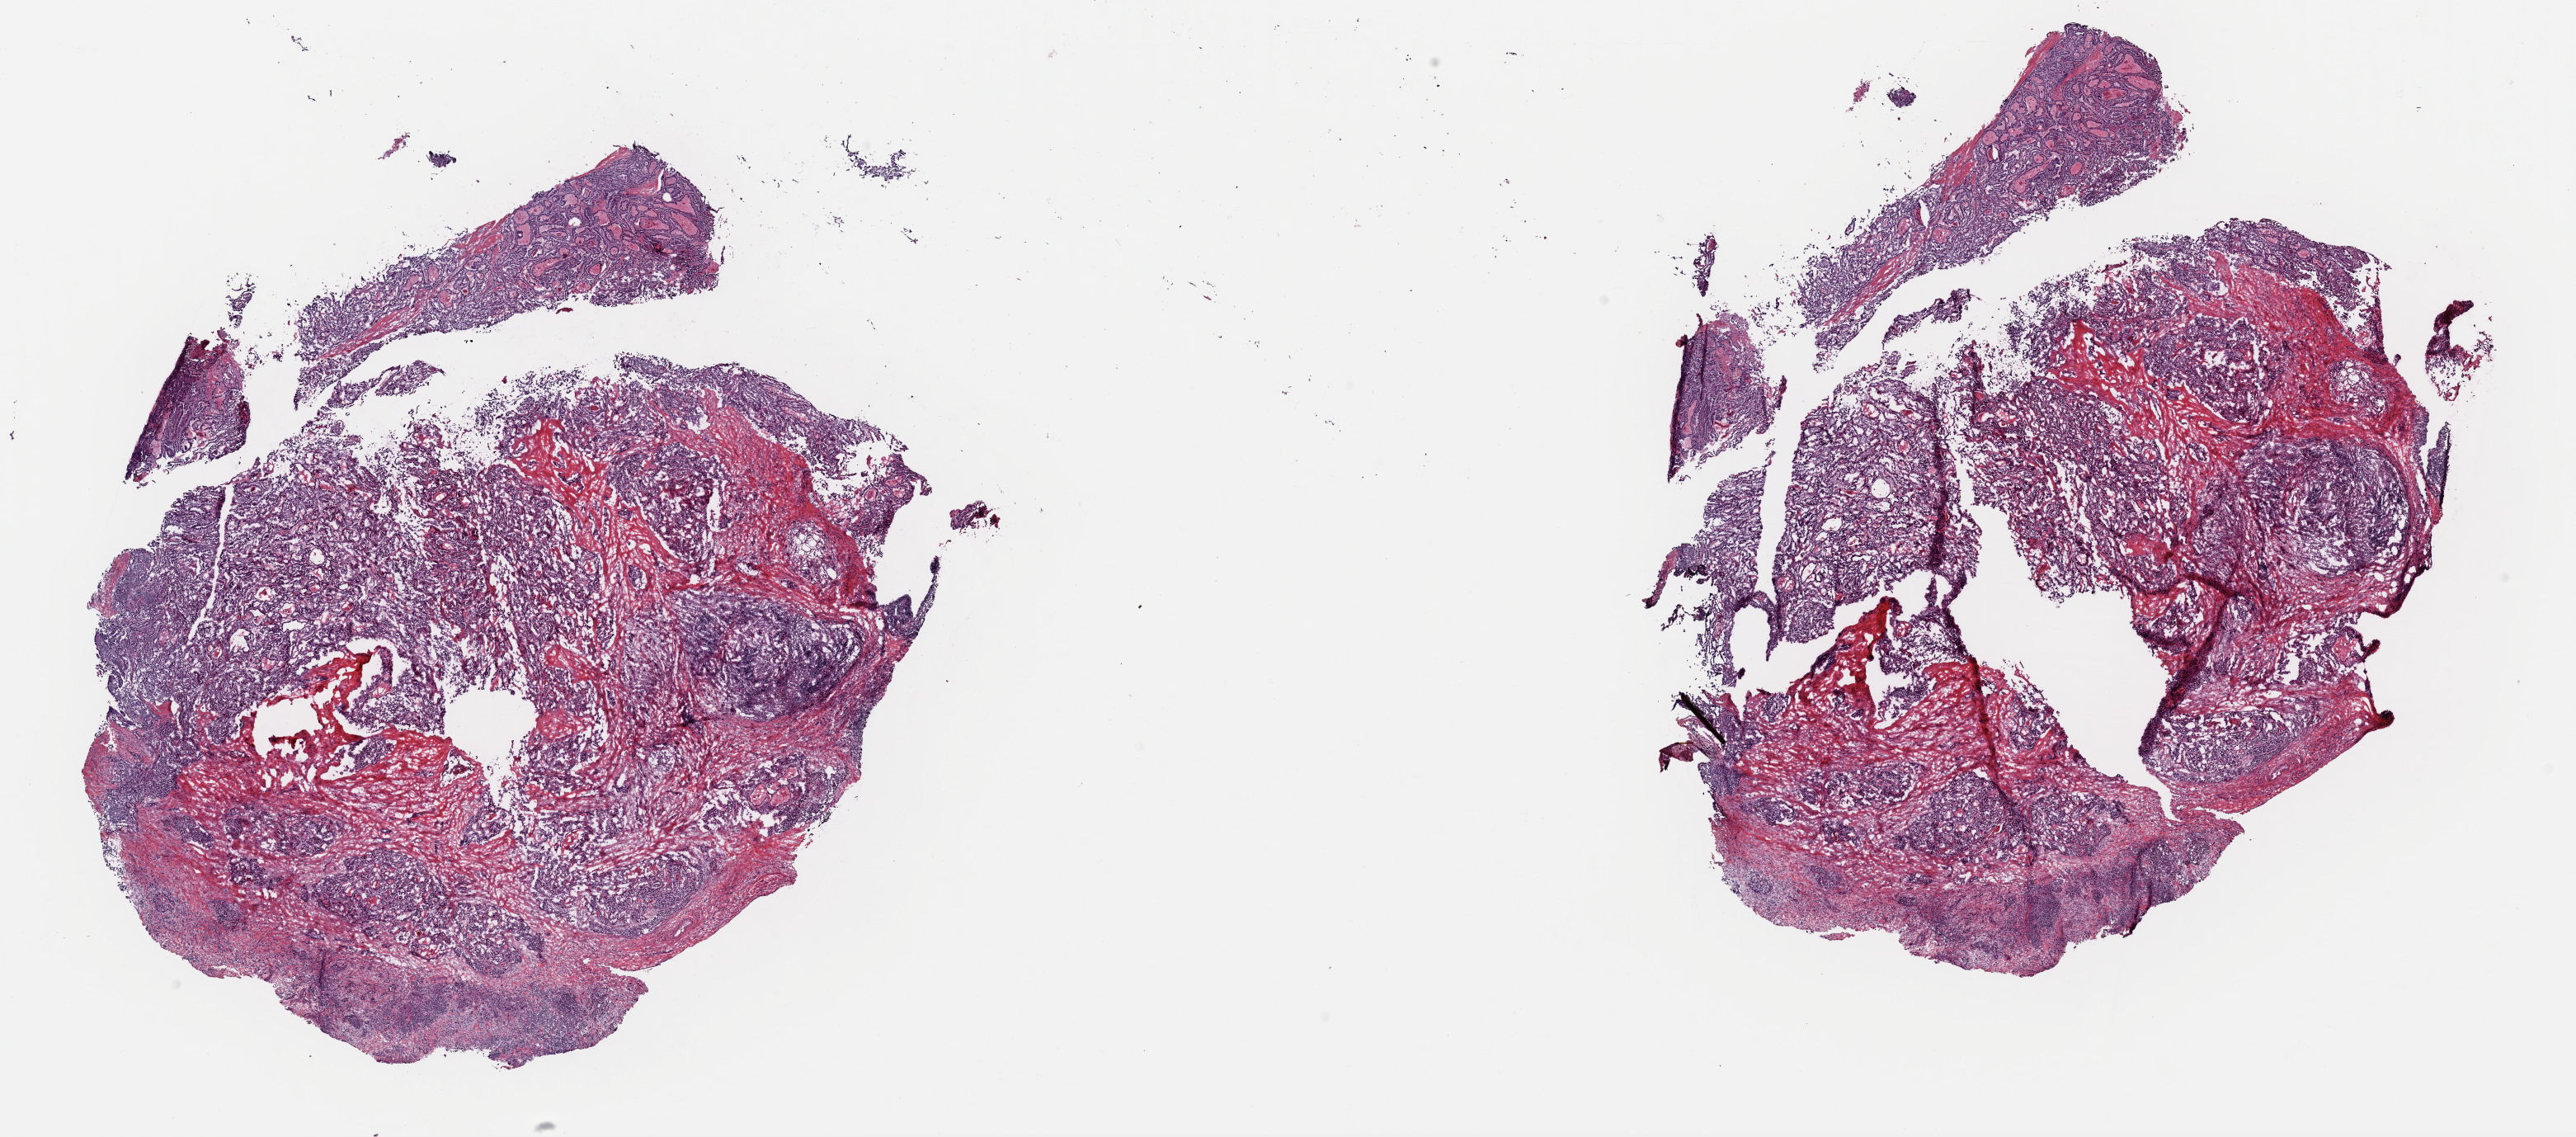
H&E whole-slide image — a low-resolution overview of the entire scanned area, about 24.7 x 10.9 mm (acquisition: 40x scan), frozen section from the top of the tissue portion, primary tumour sample from the thyroid. Female patient; age at initial diagnosis 51 years. Pathologist review of this section (percent, as recorded): tumour cells 65%, tumour nuclei 75%, normal cells 0%, stromal cells 35%, necrosis 0%. Infiltration values recorded for this section: lymphocyte infiltration 3%, monocyte infiltration 1%, neutrophil infiltration 0%.
• AJCC pathologic stage: III (7th edition)
• histologic diagnosis: Papillary carcinoma, columnar cell (thyroid gland)